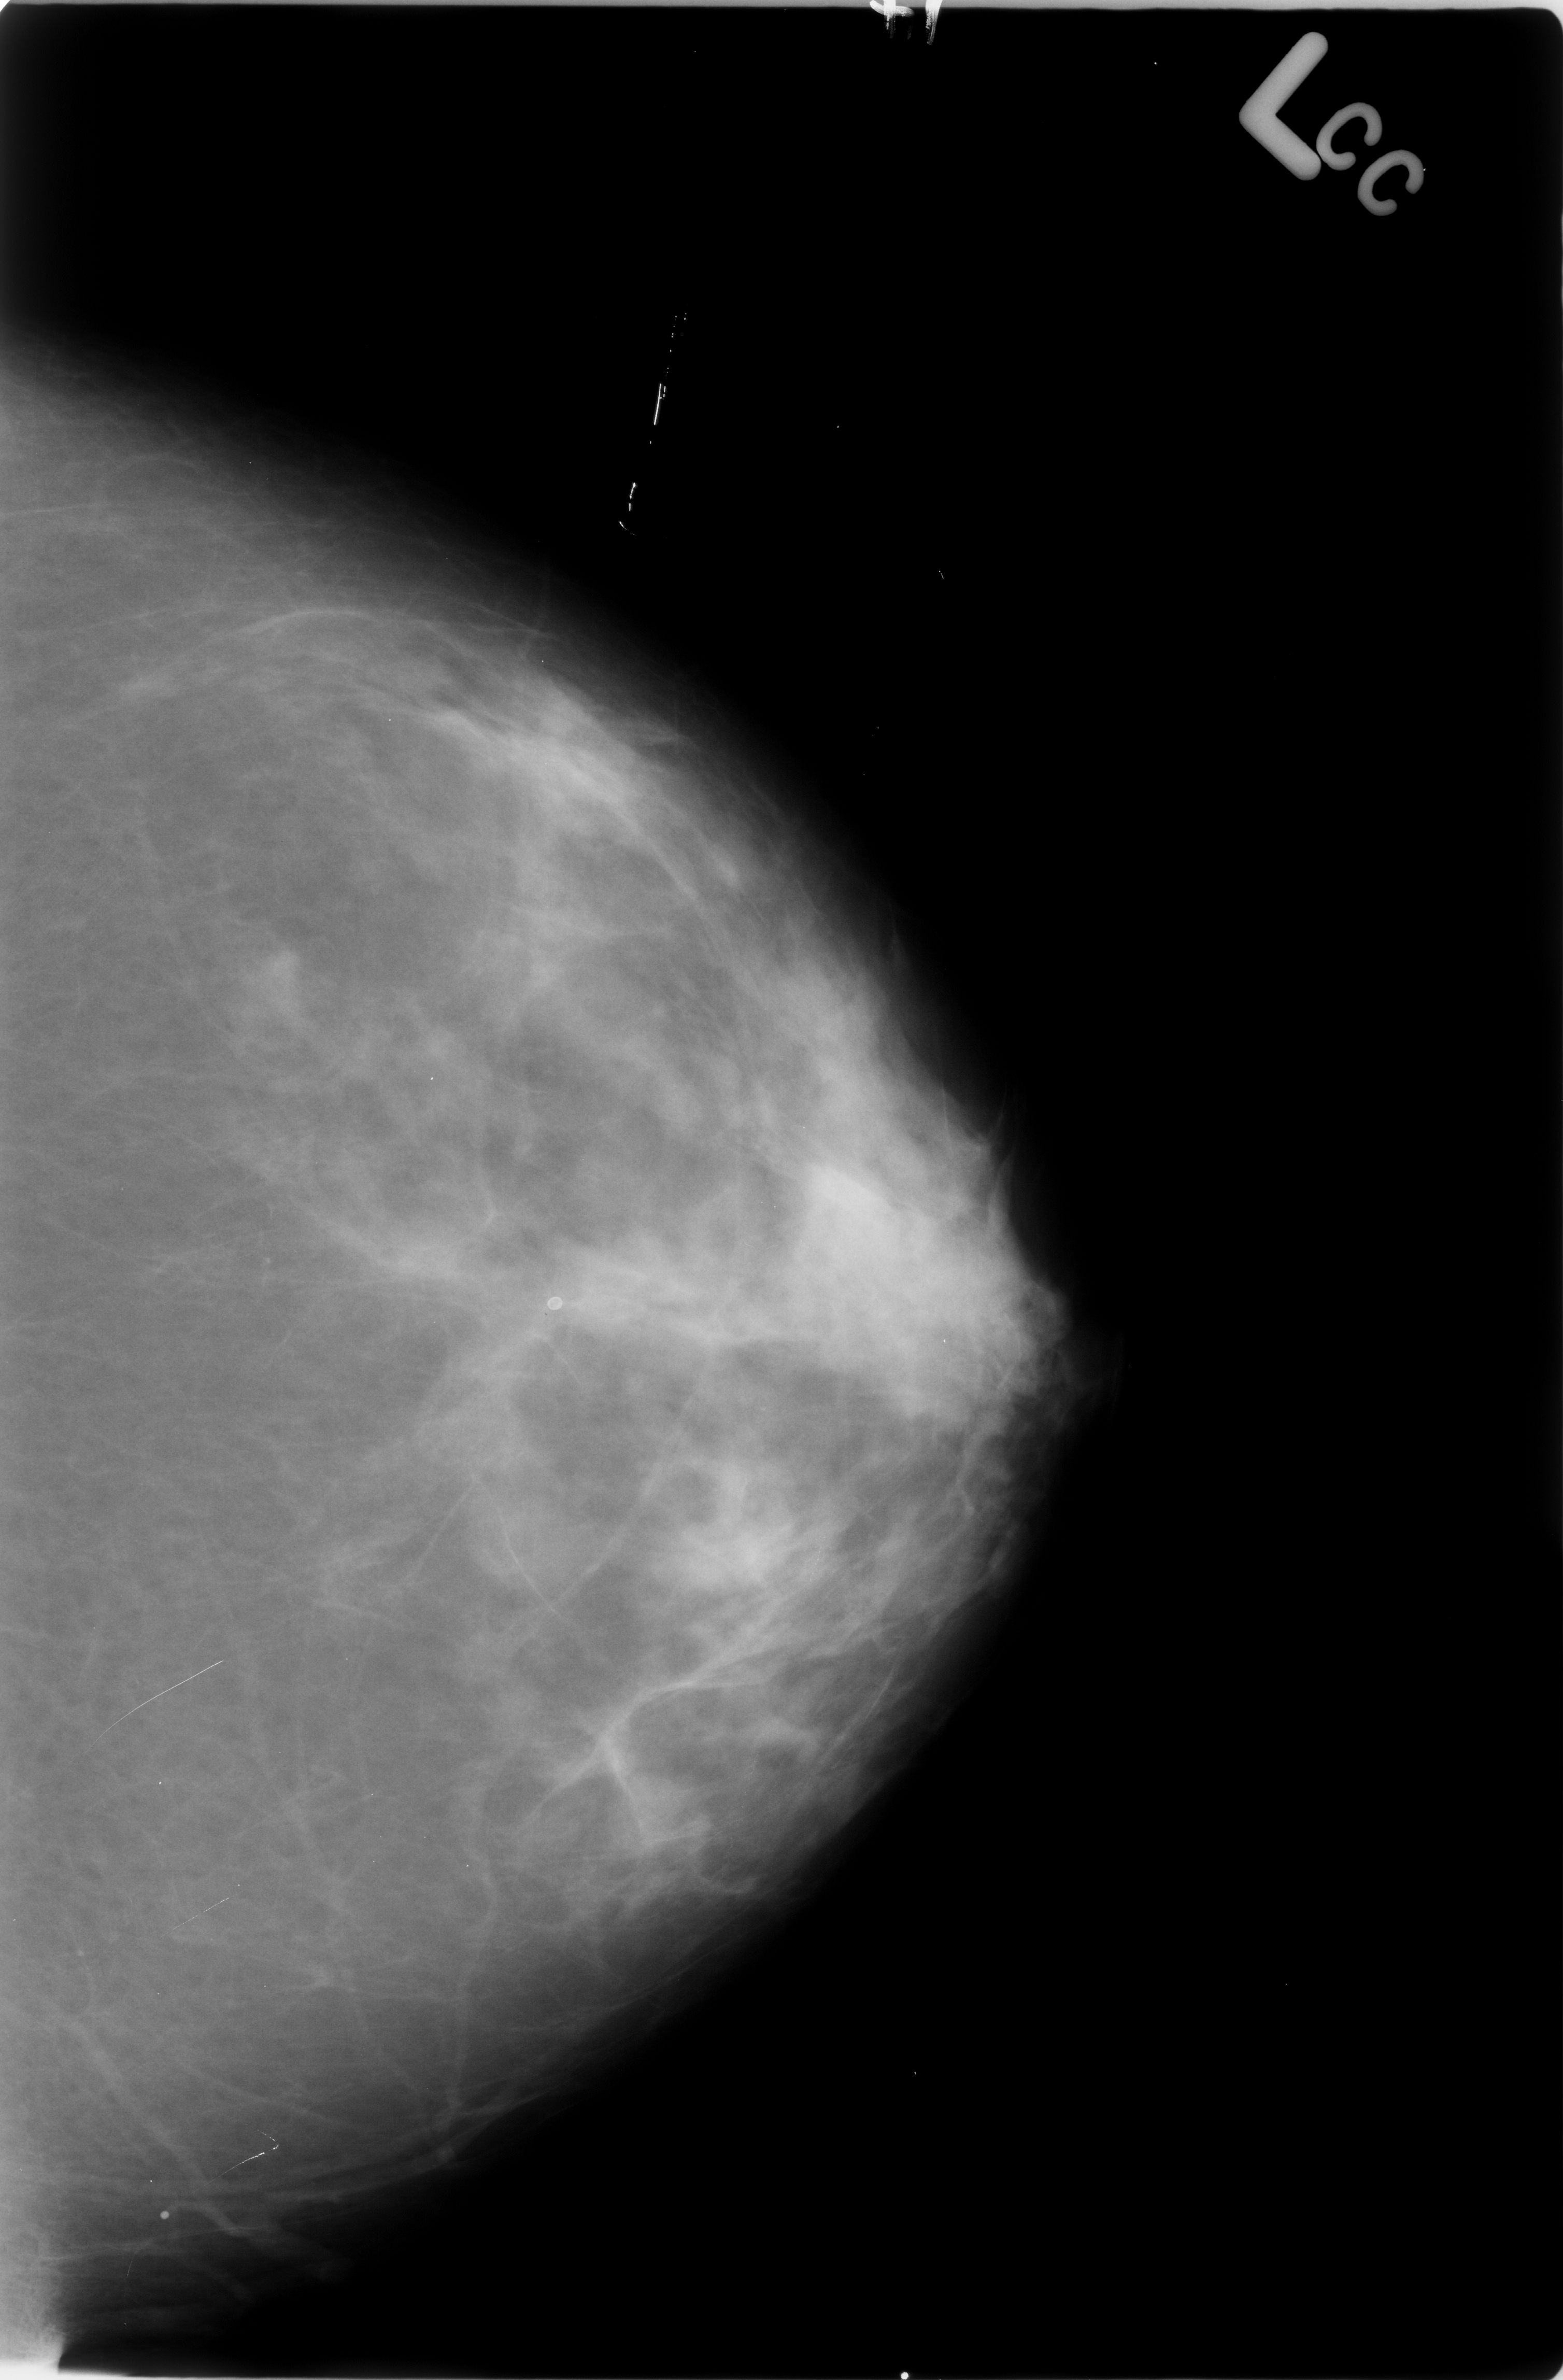
Digitized screen-film mammogram, left breast, CC view, BI-RADS breast density category 3 (scale 1–4).
Calcifications, morphology lucent center; BI-RADS assessment category 2; benign without callback (not worked up further).